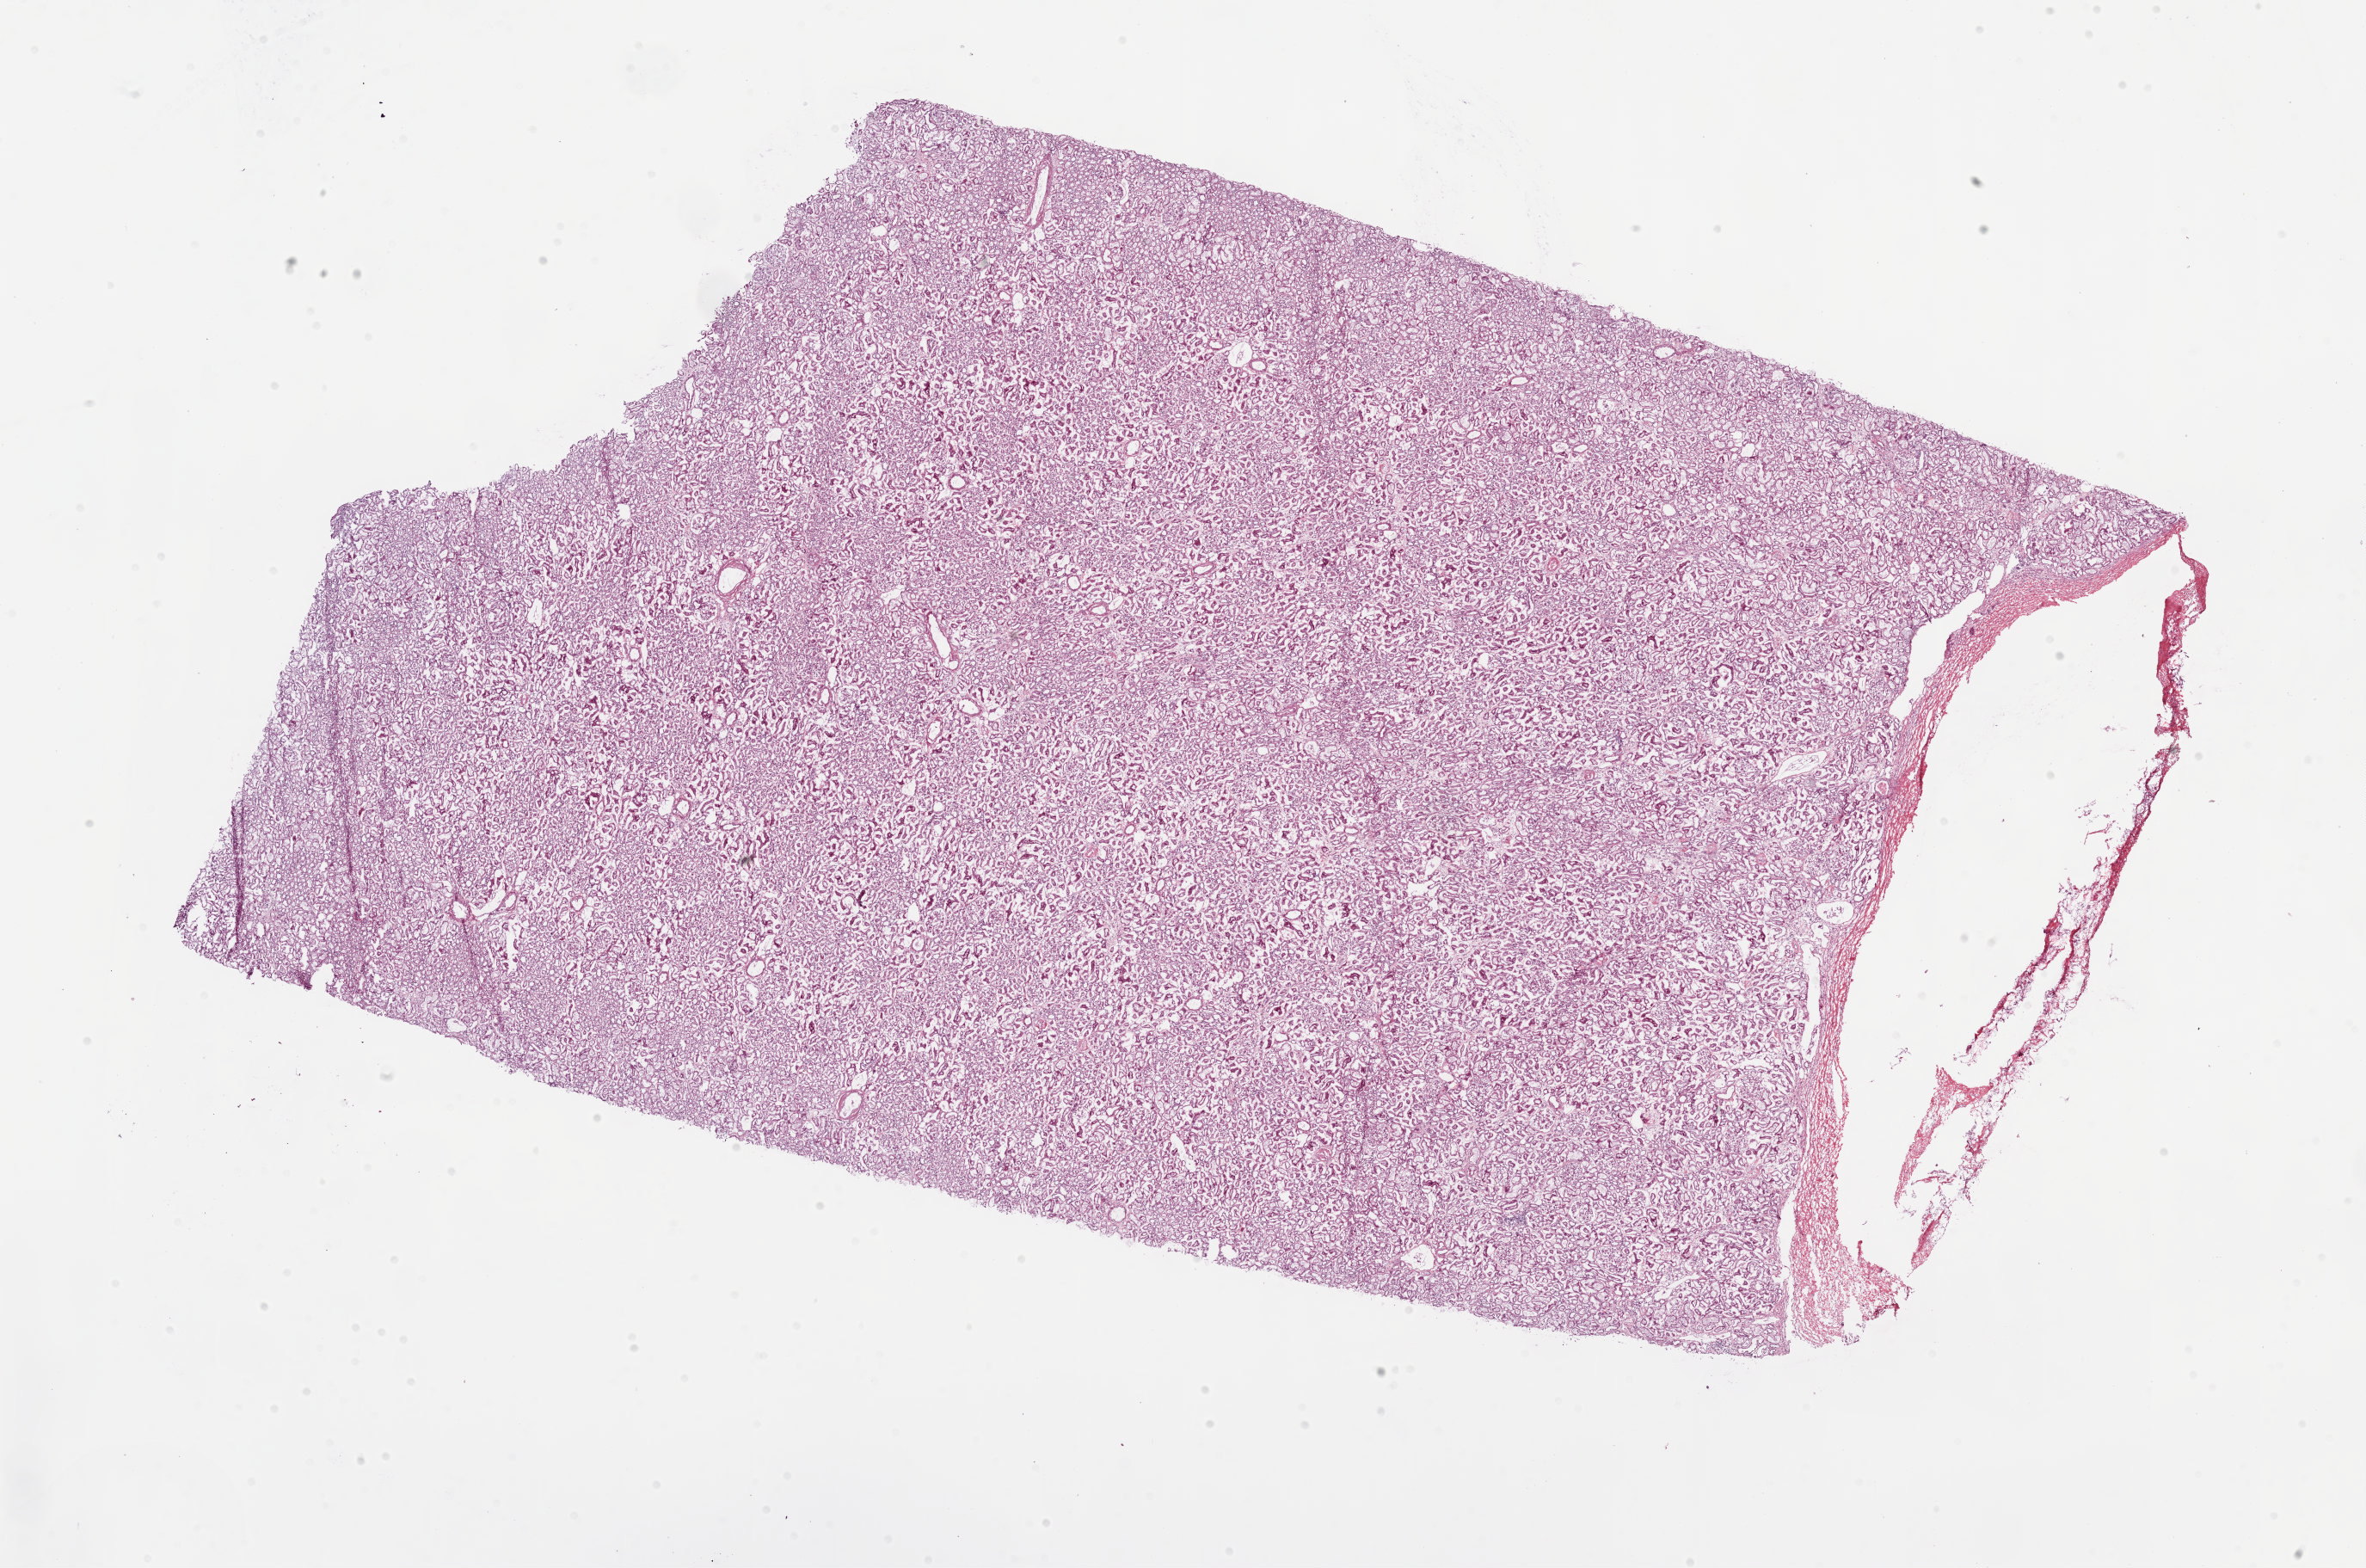
Whole-slide histology image, Hematoxylin and eosin (H&E) stained, low-resolution overview of the scanned area, about 21.8 x 14.5 mm, frozen section, sample: solid tissue normal (non-tumour tissue), kidney. Male patient; age at initial diagnosis 60 years.
This section: solid tissue normal (non-tumour) sample from the same patient. Patient diagnosis: Clear cell adenocarcinoma, NOS.